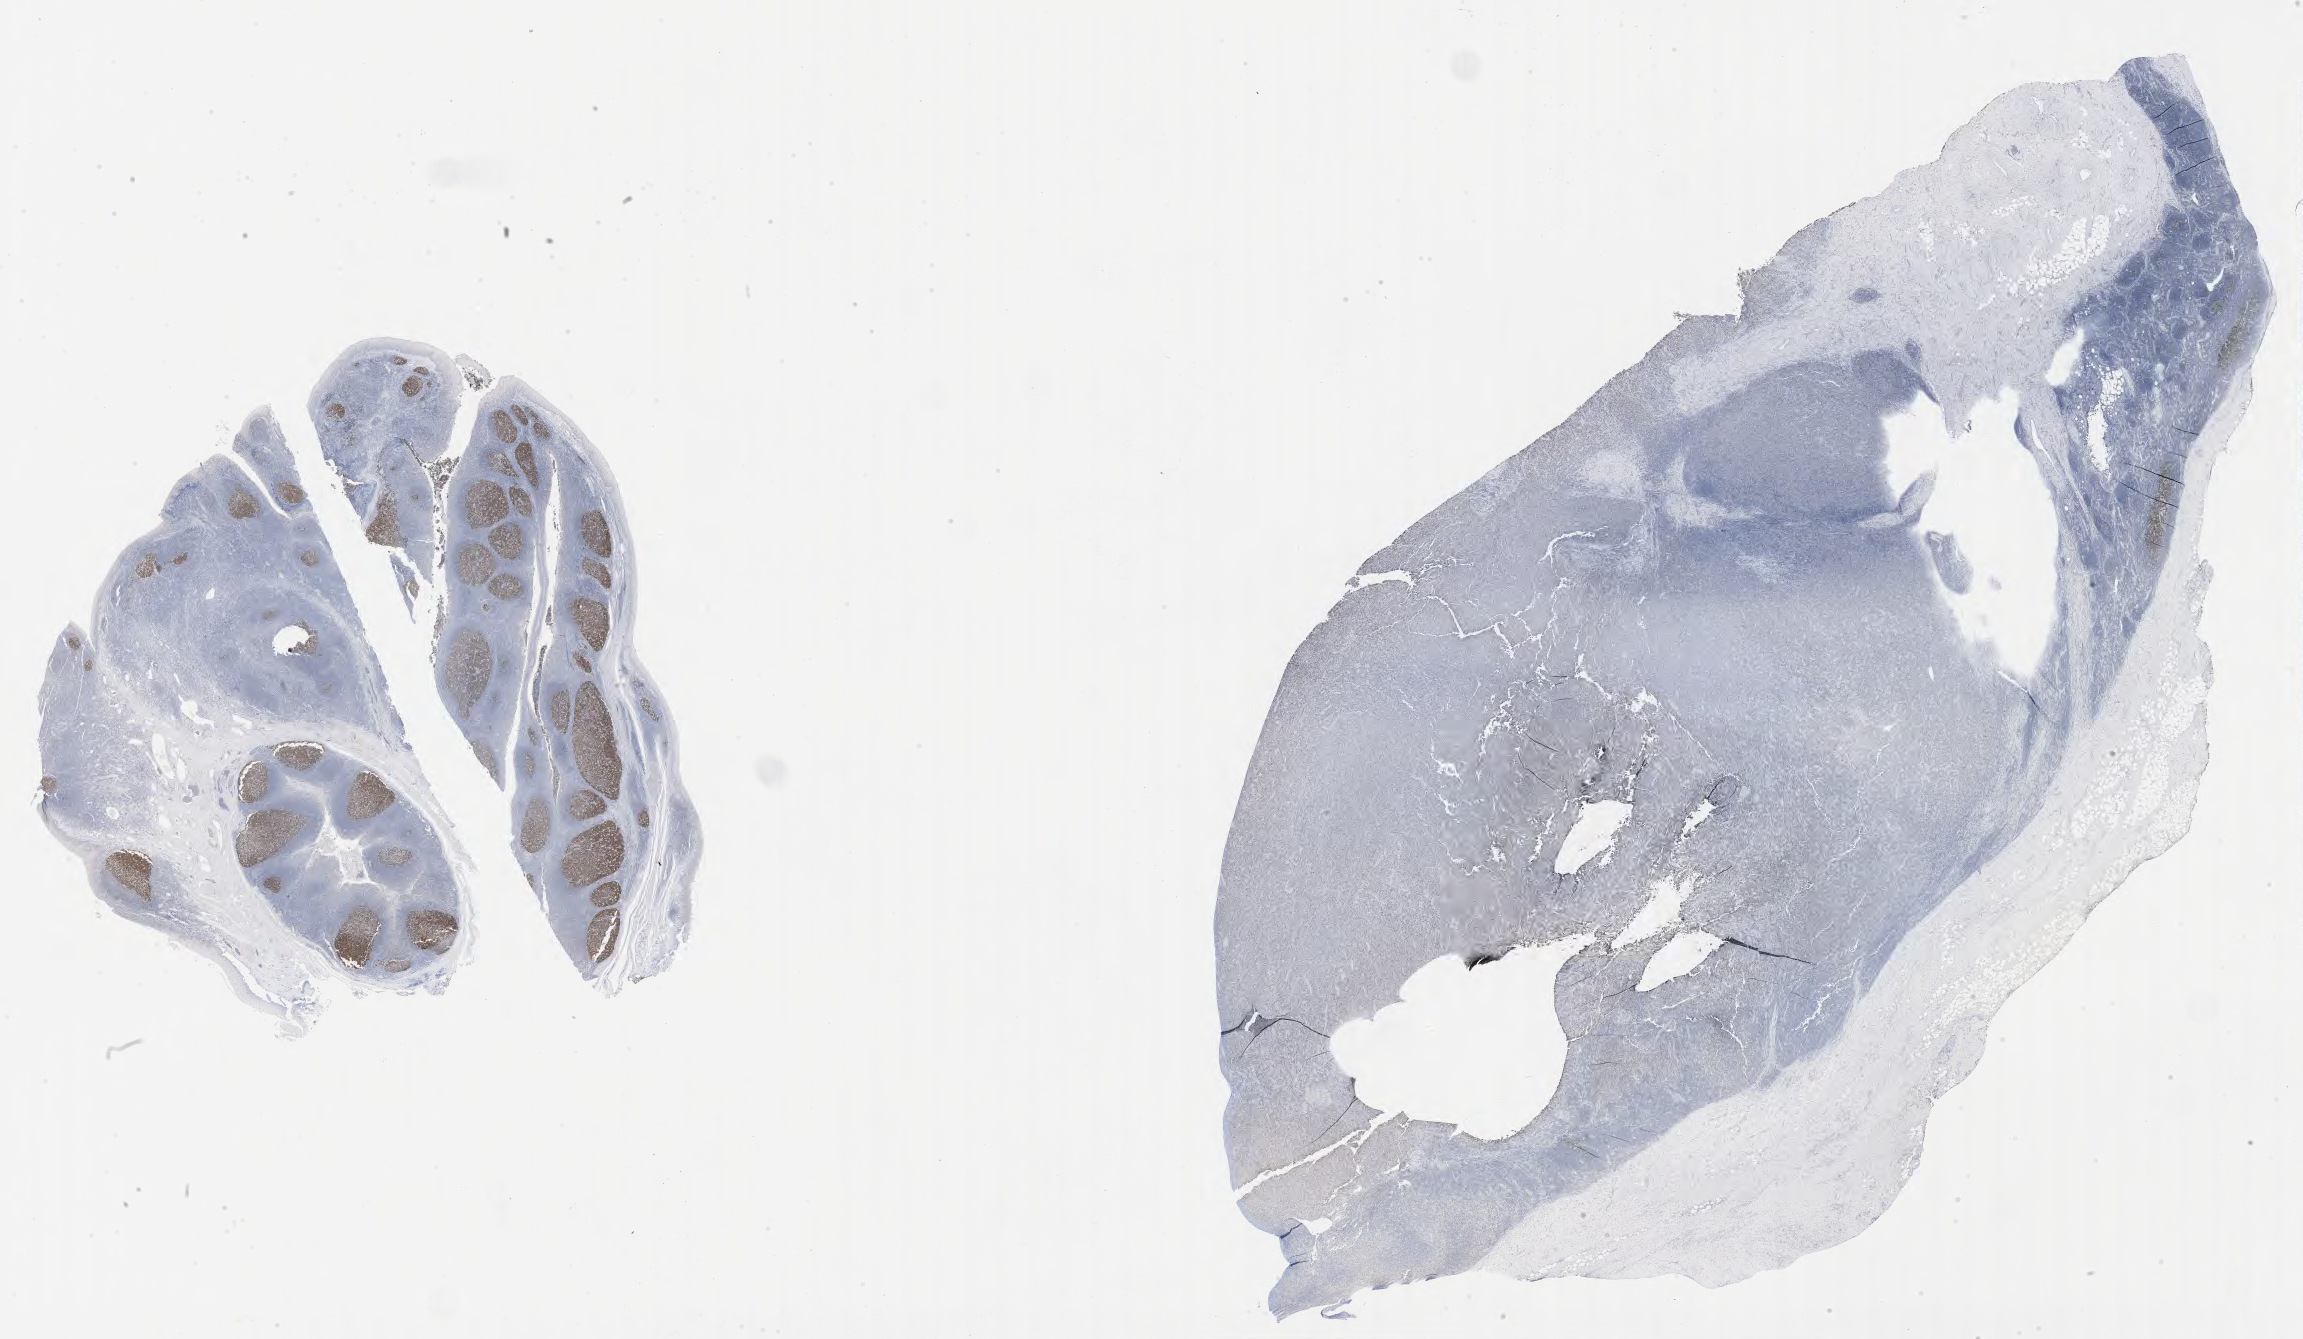
IHC for BCL6, whole-slide image — whole scanned area (about 37.2 x 21.6 mm) shown as a low-resolution overview. Specimen: tumor tissue. Anatomic site: lymph node. Male patient, aged 60.
Diagnosis: Diffuse large B-cell lymphoma, NOS.